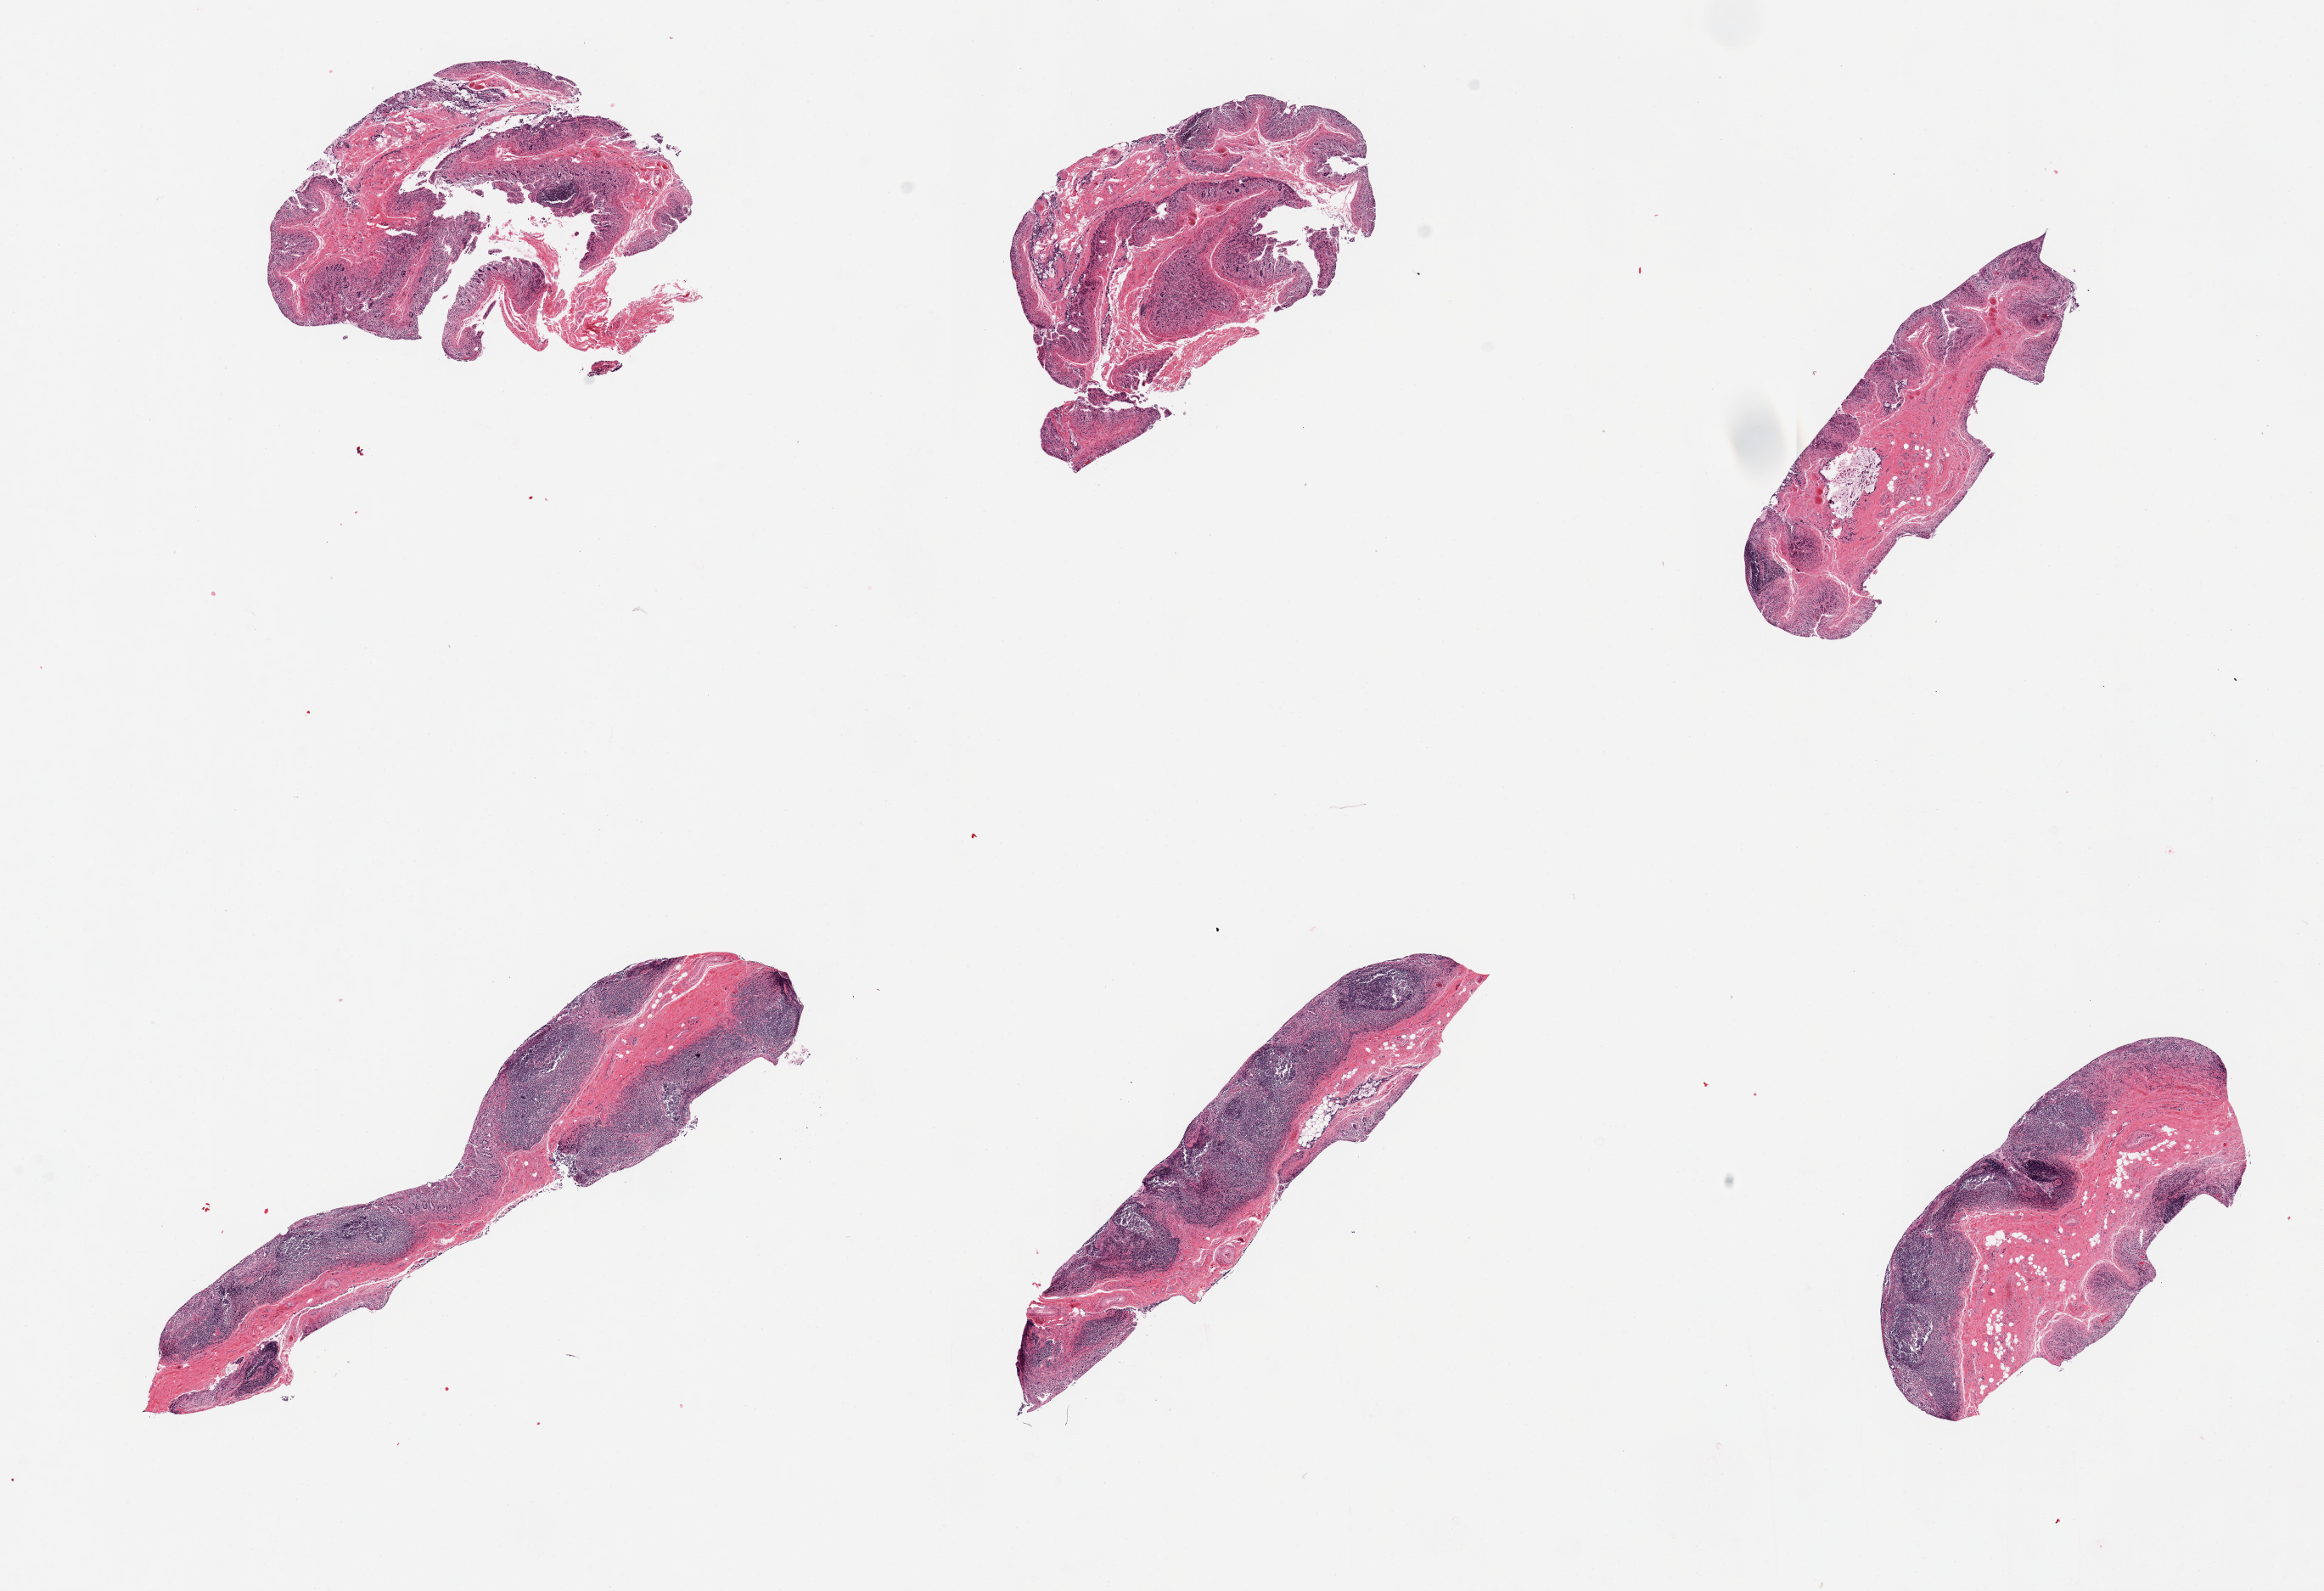
Digitized H&E-stained section, shown as a low-resolution overview of the whole scanned area (about 21.7 x 14.8 mm, acquisition: 20x scan). PAXgene-fixed paraffin-embedded (PFPE) section. Target tissue: ileum. Donor tissue sample. Donor: female.
Review note (as recorded): 6 pieces; autolyzed mucosa, 3 of 6 pieces have abundant lymphoid tissue.